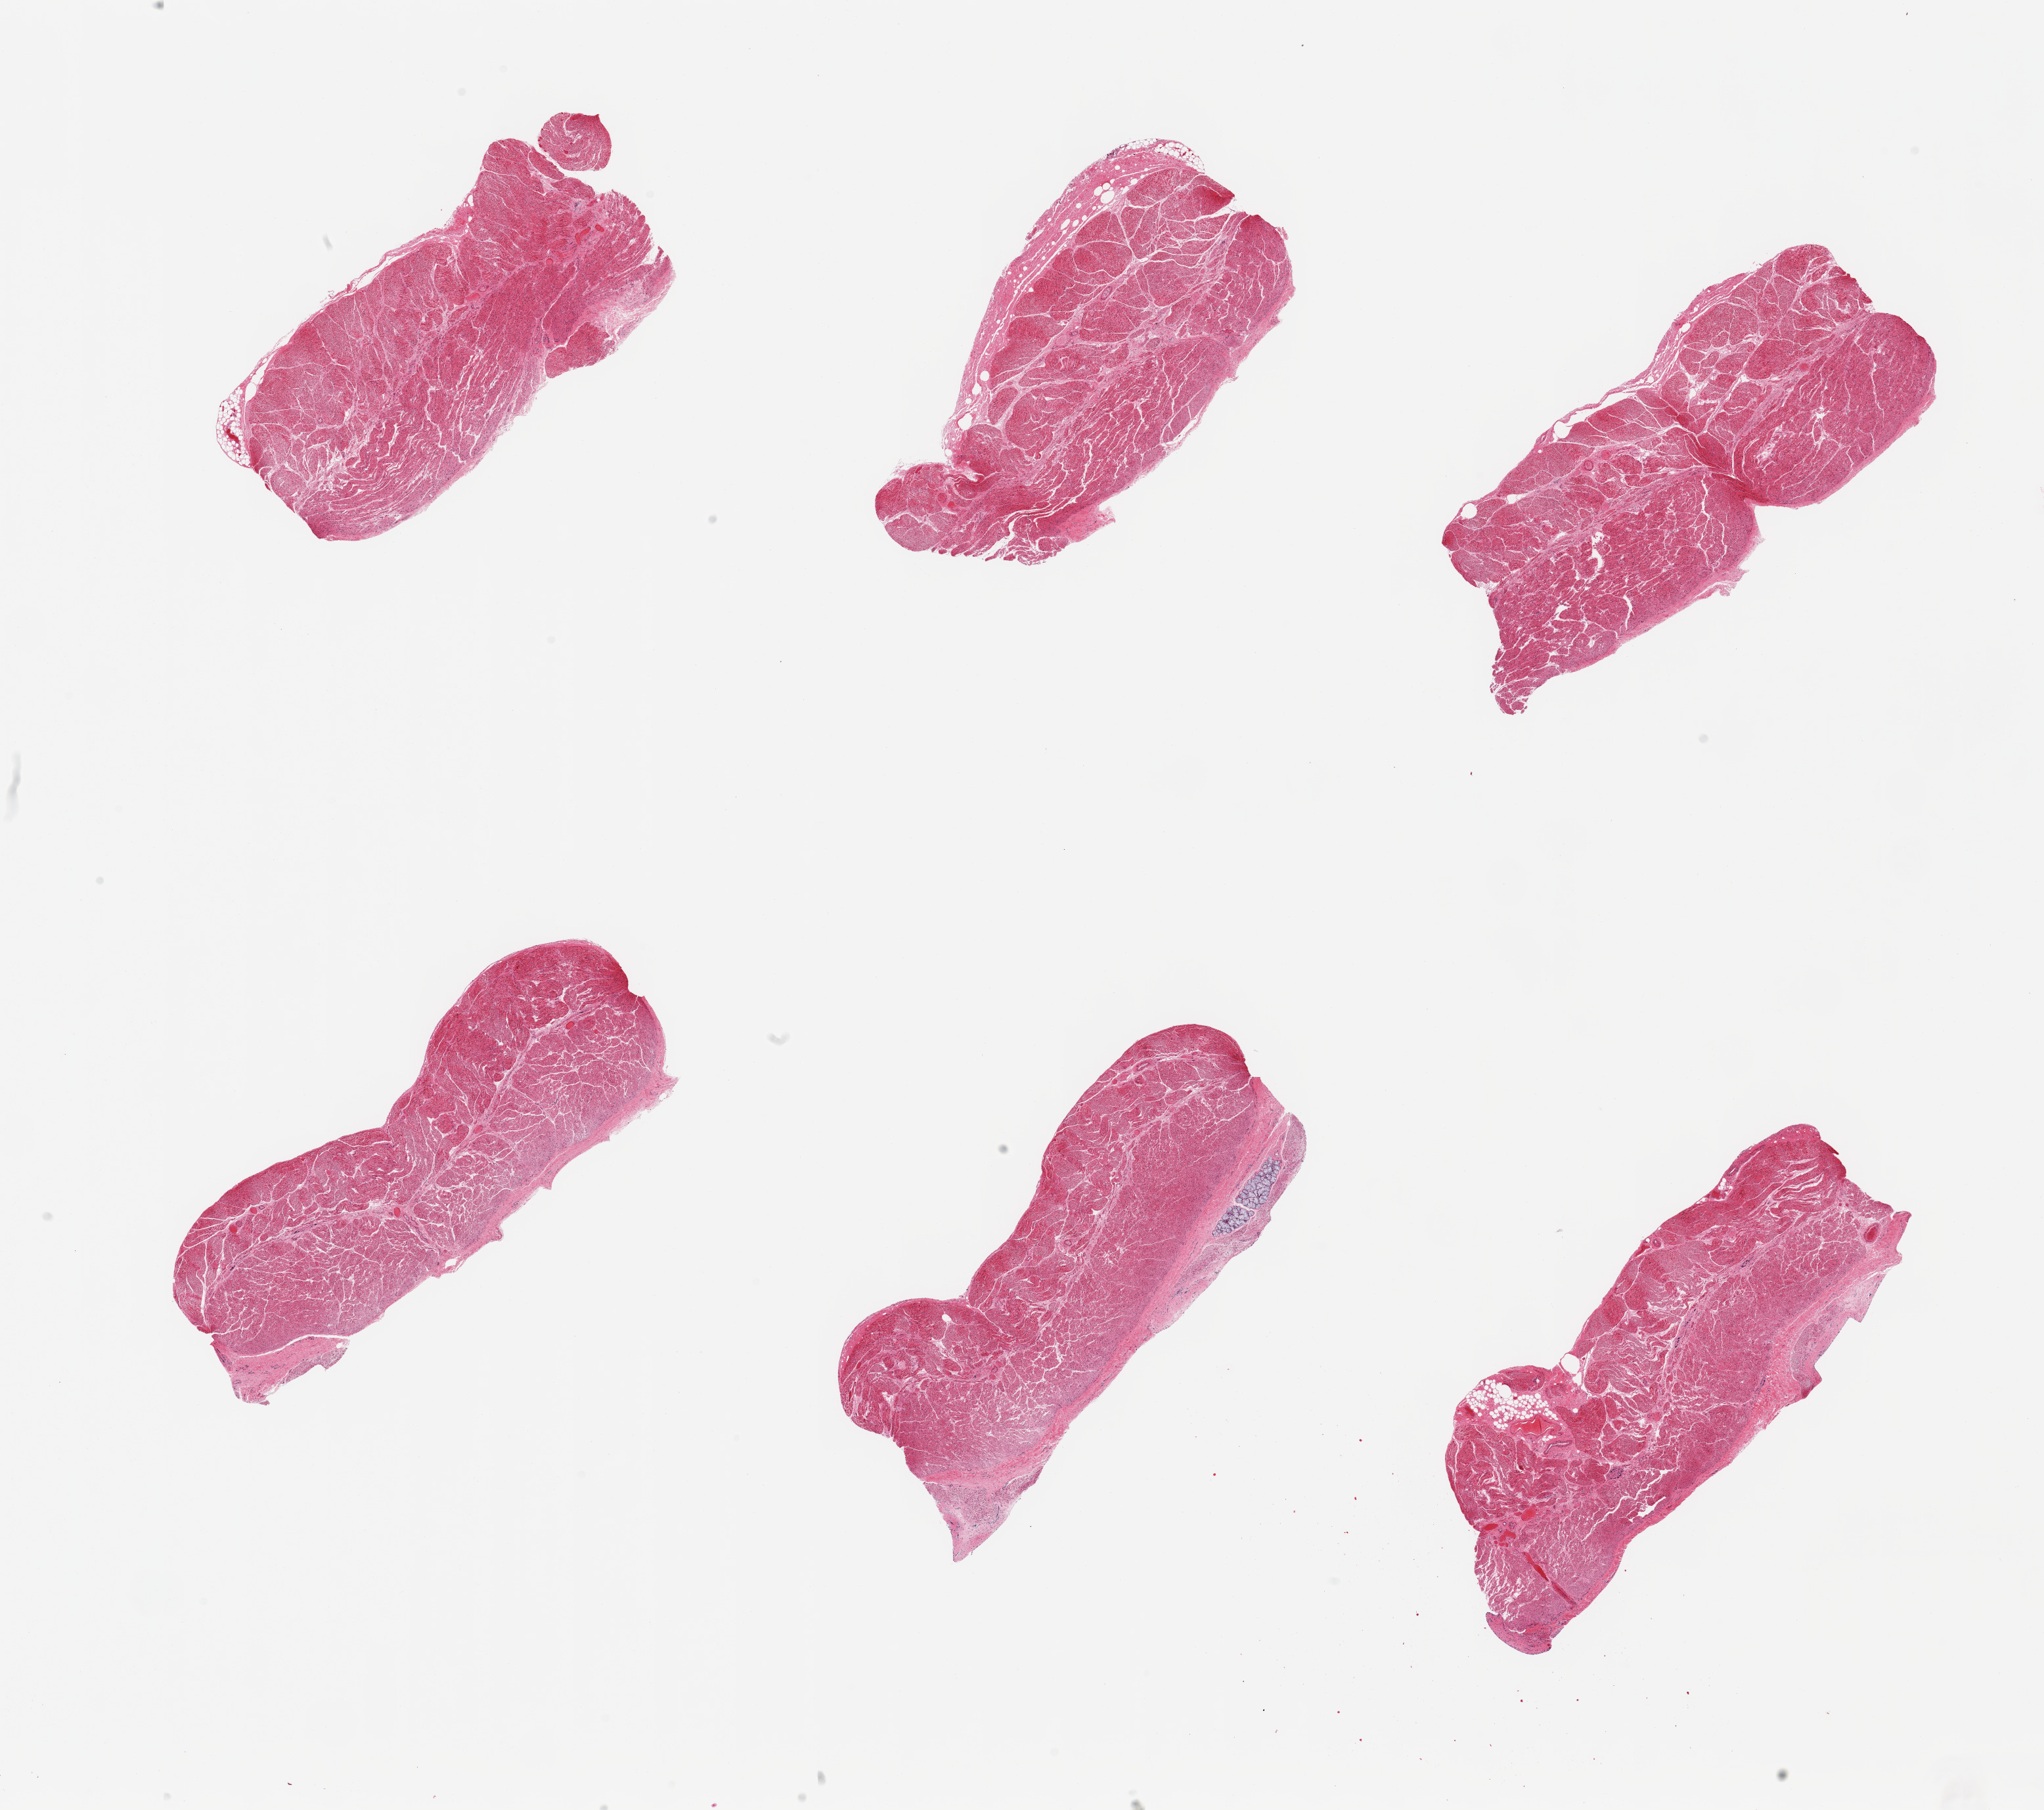
Digitized H&E-stained section, a low-resolution overview of the entire scanned area, about 24.6 x 21.8 mm (slide scanned at 20x); PAXgene-fixed paraffin-embedded (PFPE) section; target tissue: esophageal muscle; tissue donor sample. Donor sex: male.
Reviewer comment on this tissue sample: 6 pieces; target muscularis and focus of submucosal glands.